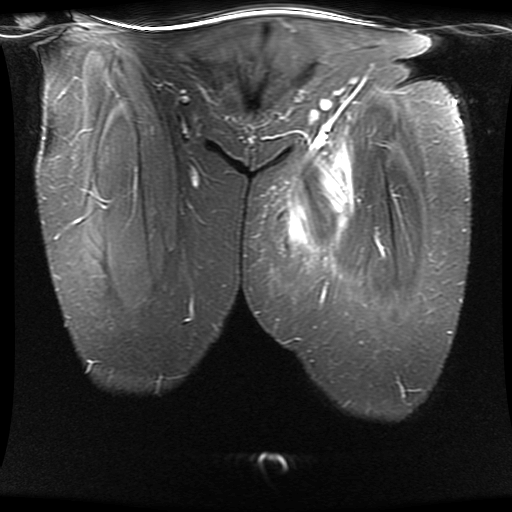
MRI of an extremity soft-tissue mass, one coronal slice. Slice 5 of 30 in the series (ordered by position). STIR. 5 mm slice thickness. 512 × 512 image matrix, field of view 460 × 460 mm. Female patient. Case-level facts recorded for this patient, not image findings: histological type: myxofibrosarcoma; grade: intermediate; site of the primary tumour: left thigh.
Structures marked on this image (manually delineated by an expert):
- gross tumour volume including surrounding oedema: box from (x=287, y=142) to (x=354, y=251) px
- gross tumour volume (mass): (x=294, y=162)–(x=346, y=241)